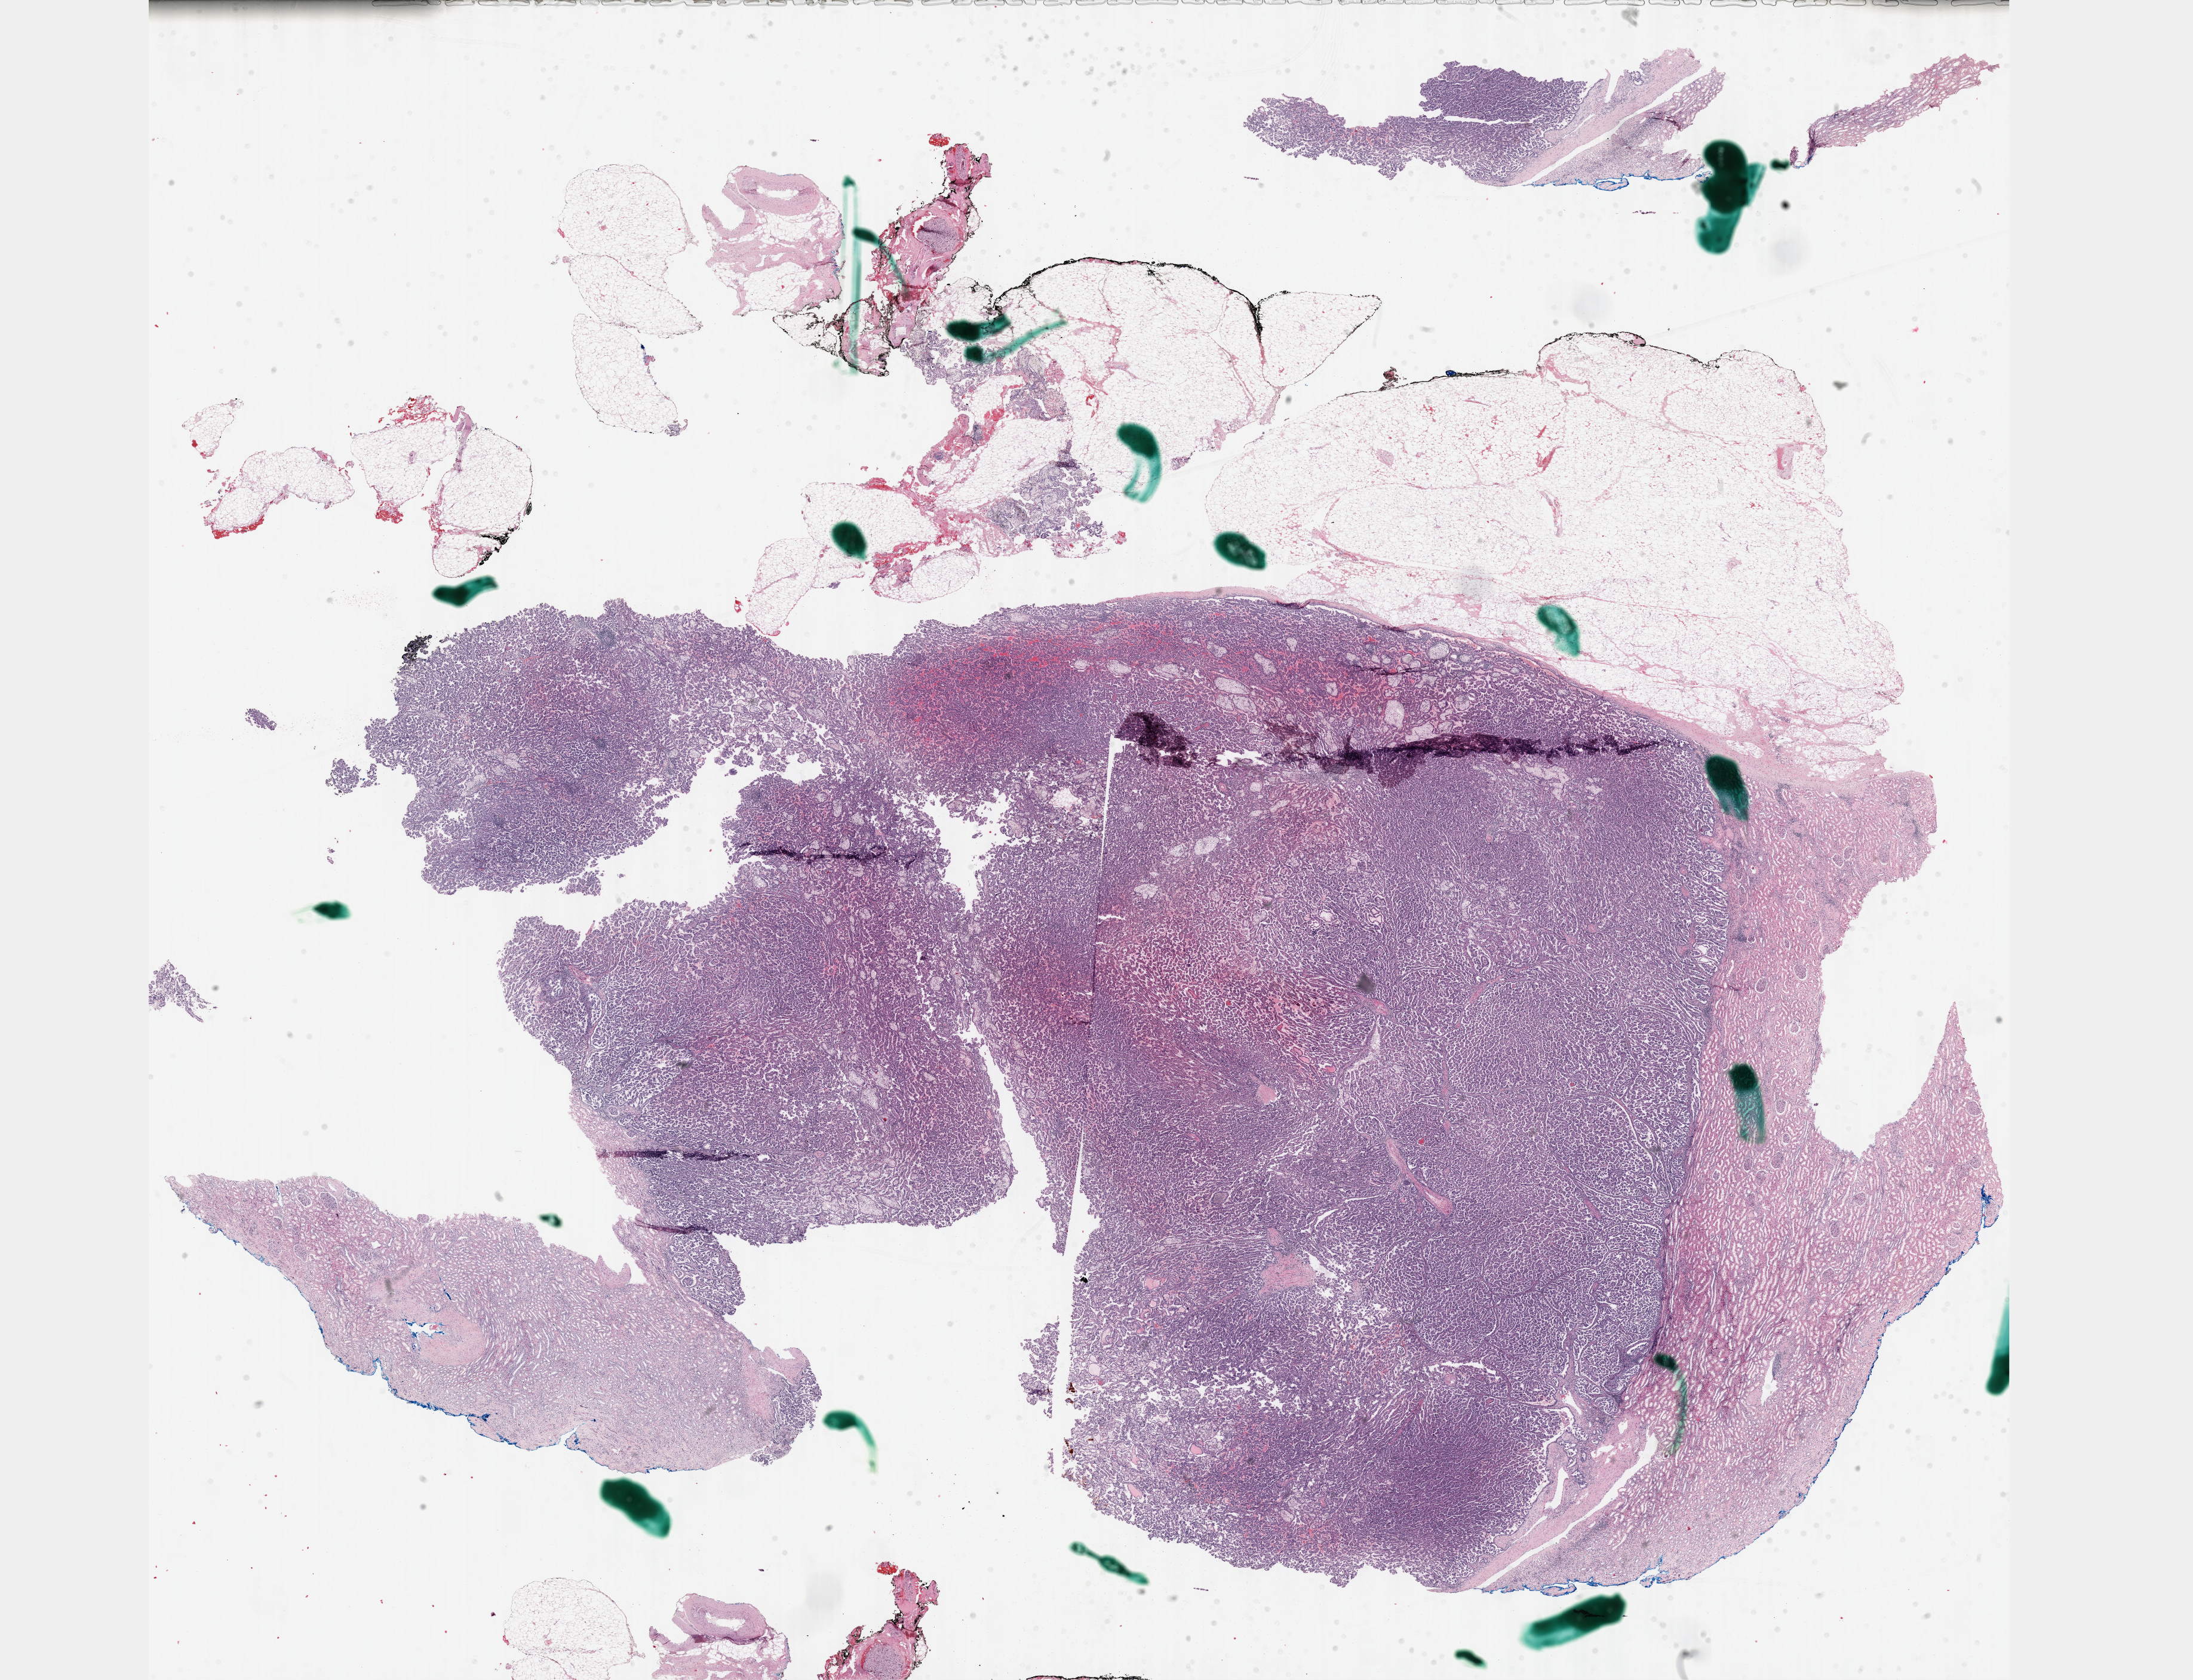
H&E-stained whole-slide image — low-resolution overview of the scanned area, about 29.7 x 22.7 mm (acquisition: 40x scan); formalin-fixed paraffin-embedded (FFPE) diagnostic section; kidney, primary tumour sample. Patient: male, age at initial diagnosis 65 years.
- pathologic diagnosis: Papillary adenocarcinoma, NOS
- AJCC pathologic stage: I